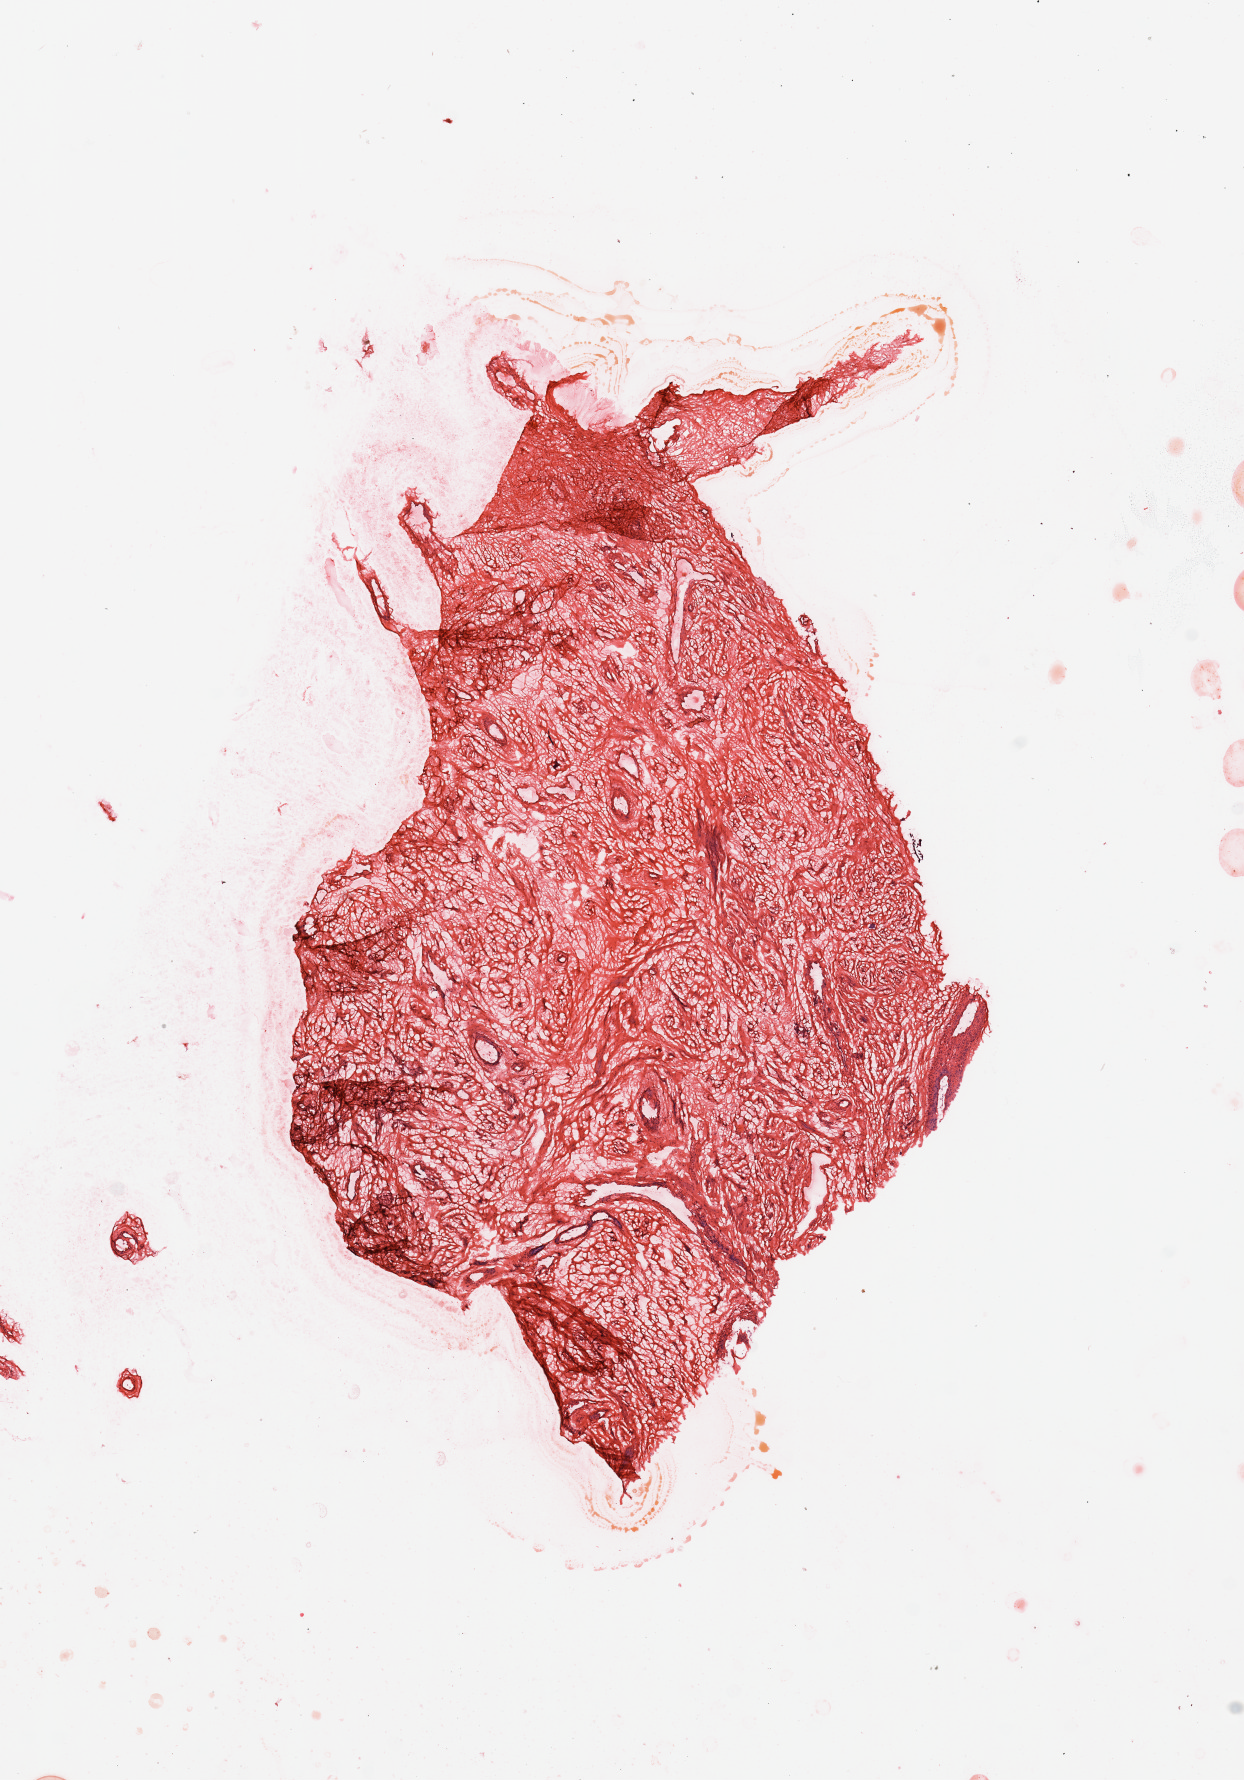
Whole-slide histology image, Hematoxylin and eosin (H&E) stained — shown as a low-resolution overview of the whole scanned area (about 9.8 x 14.1 mm, slide scanned at 20x), uterus, normal (non-tumour) tissue. Female, 44 y/o.
This section: normal (non-tumour) tissue from the same patient. Patient diagnosis: Endometrioid adenocarcinoma, NOS.